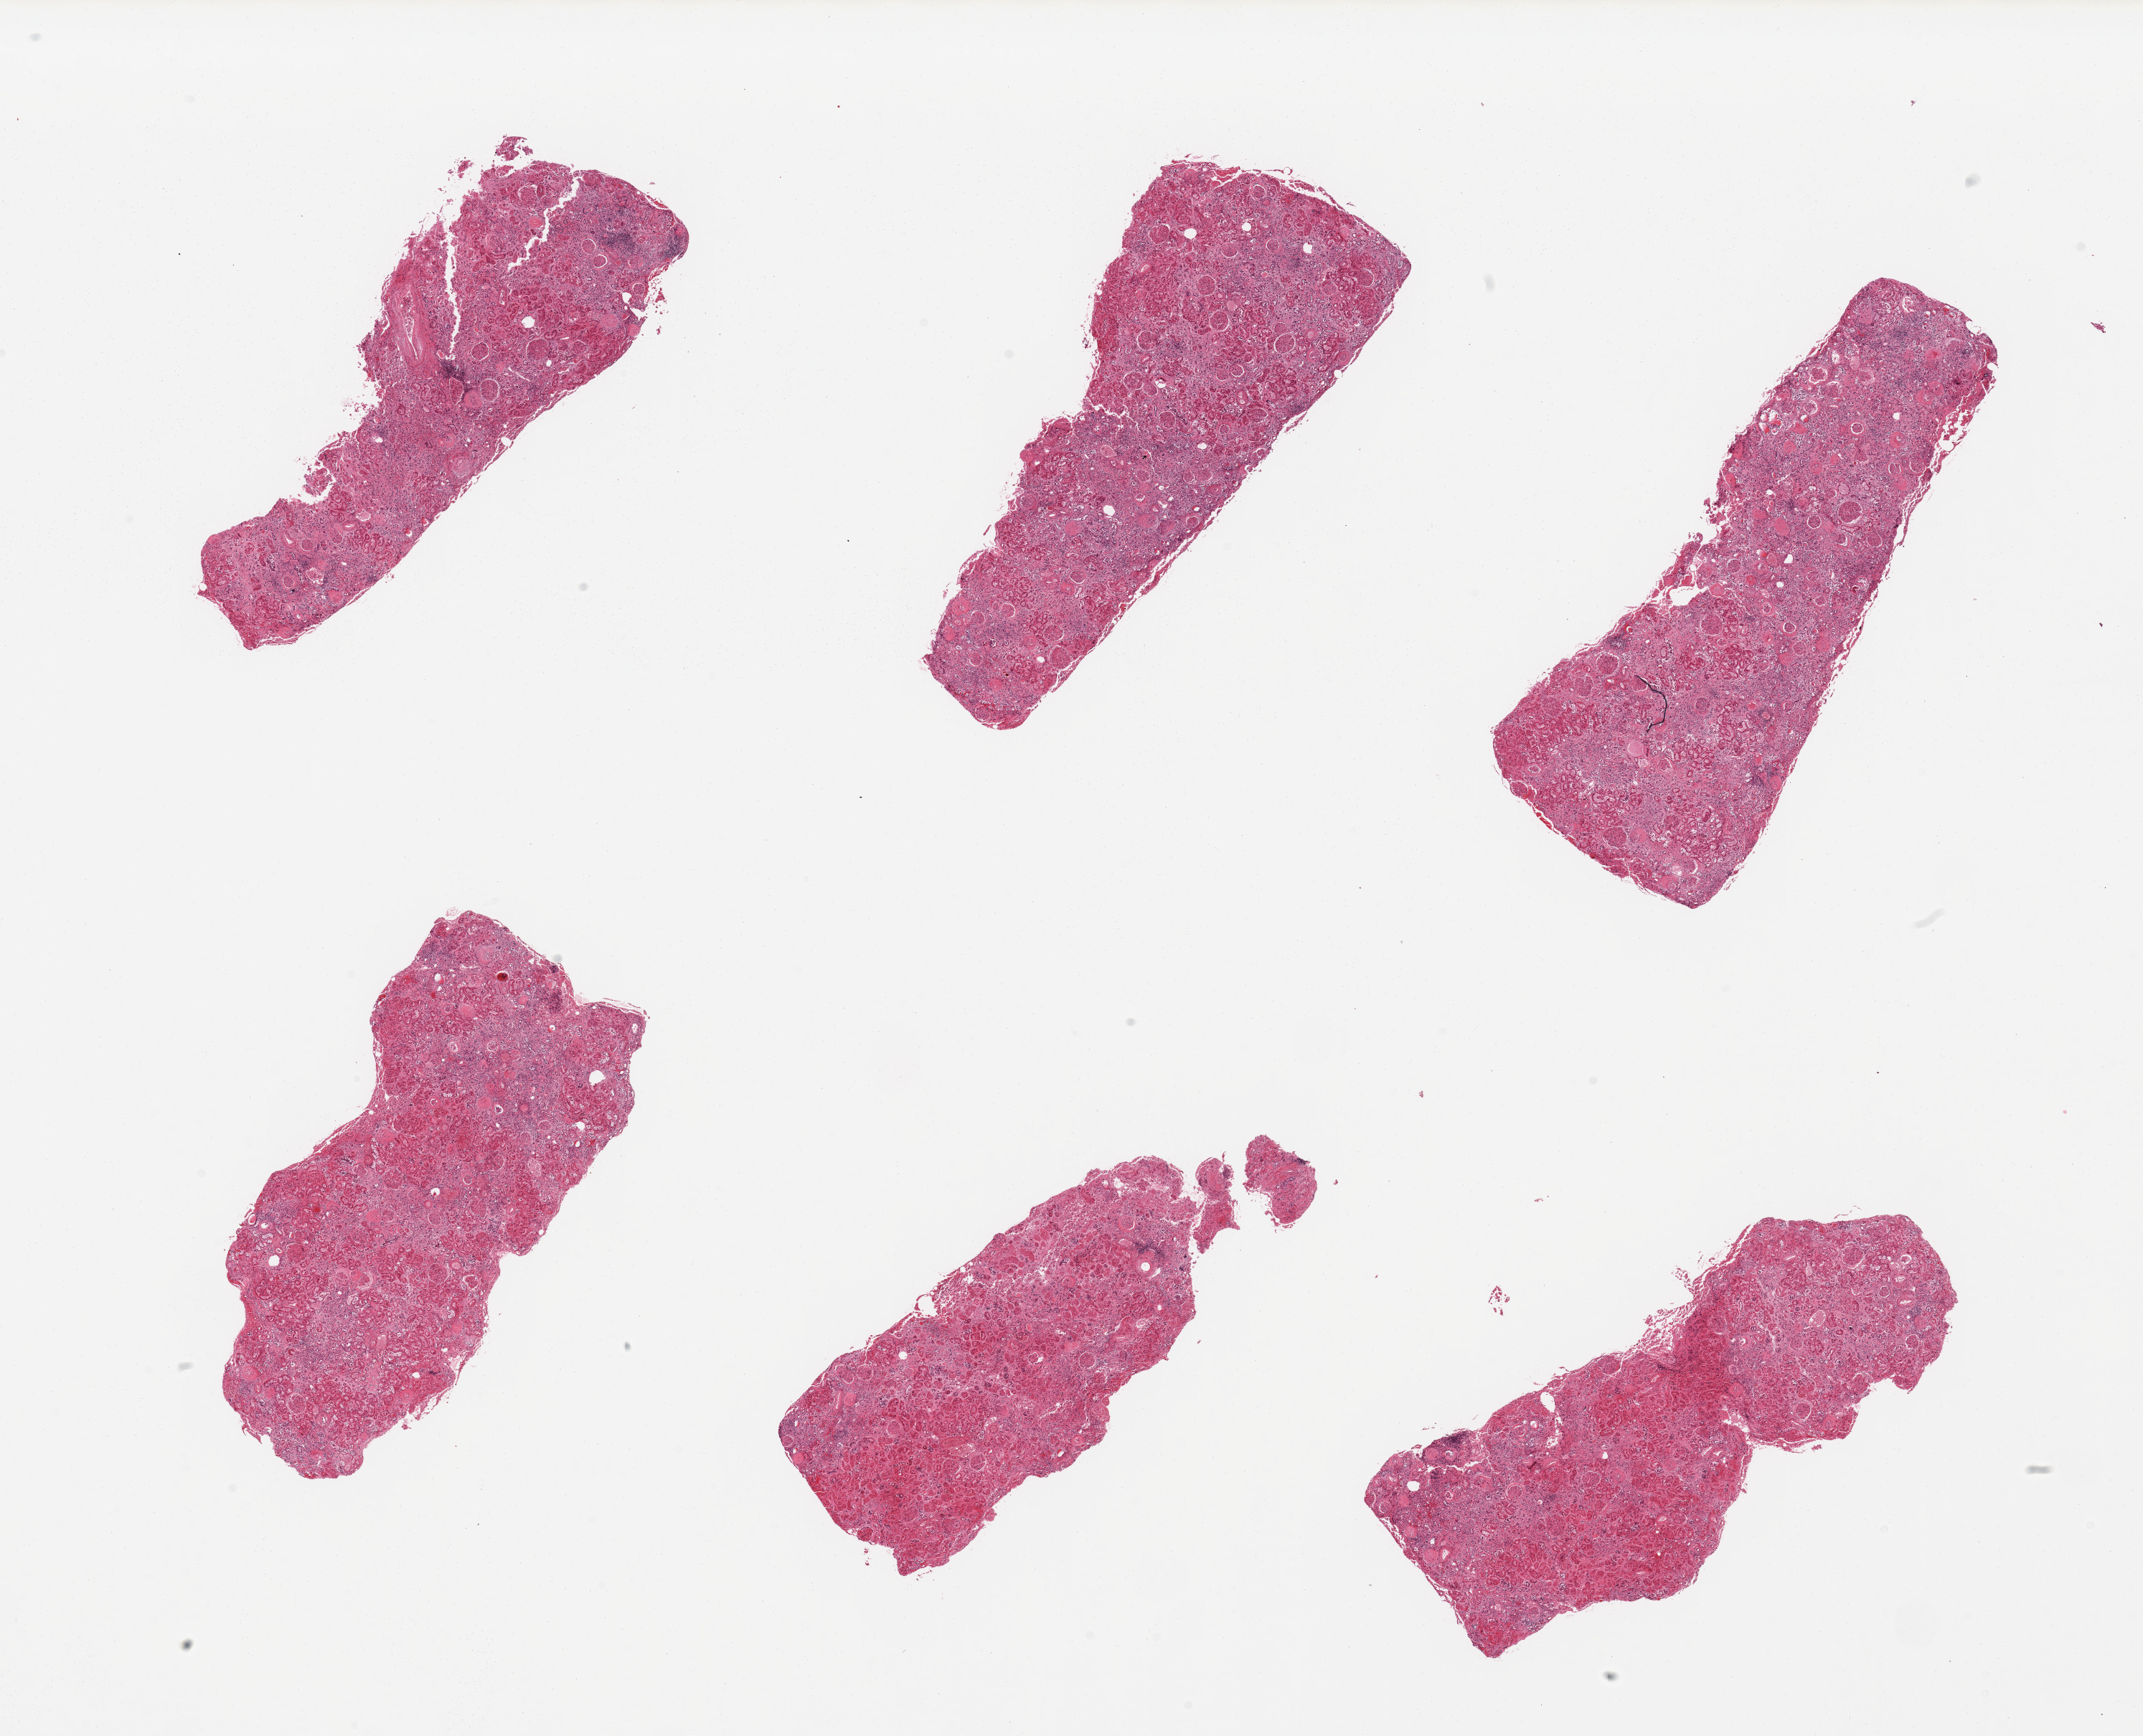
Whole-slide image, H&E stain, low-resolution overview of the scanned area, about 23.6 x 19.1 mm; PAXgene-fixed, paraffin-embedded tissue; sampled site (target tissue): renal cortex; donor tissue sample.
Review note (as recorded): 6 pieces, glomeruli present, all sections.